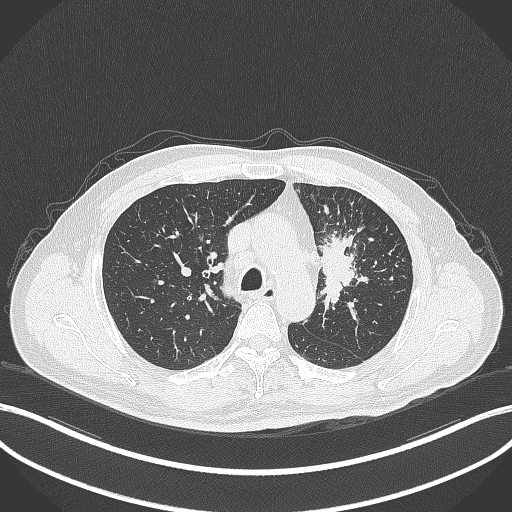
Chest CT, one axial slice; slice 246 of 386 in the series (ordered by position); lung window (W 1500 / L -600 HU); 1 mm slice thickness; 512 × 512 image matrix, field of view 400 × 400 mm. Male patient, age 69 years. From the clinical record (not read from this slice): clinical TNM (as recorded): T2a N2 M0.
Annotated regions visible in this slice (bounding box drawn by a radiologist):
- lung tumour (recorded histology: adenocarcinoma): box from (x=318, y=221) to (x=369, y=309) px